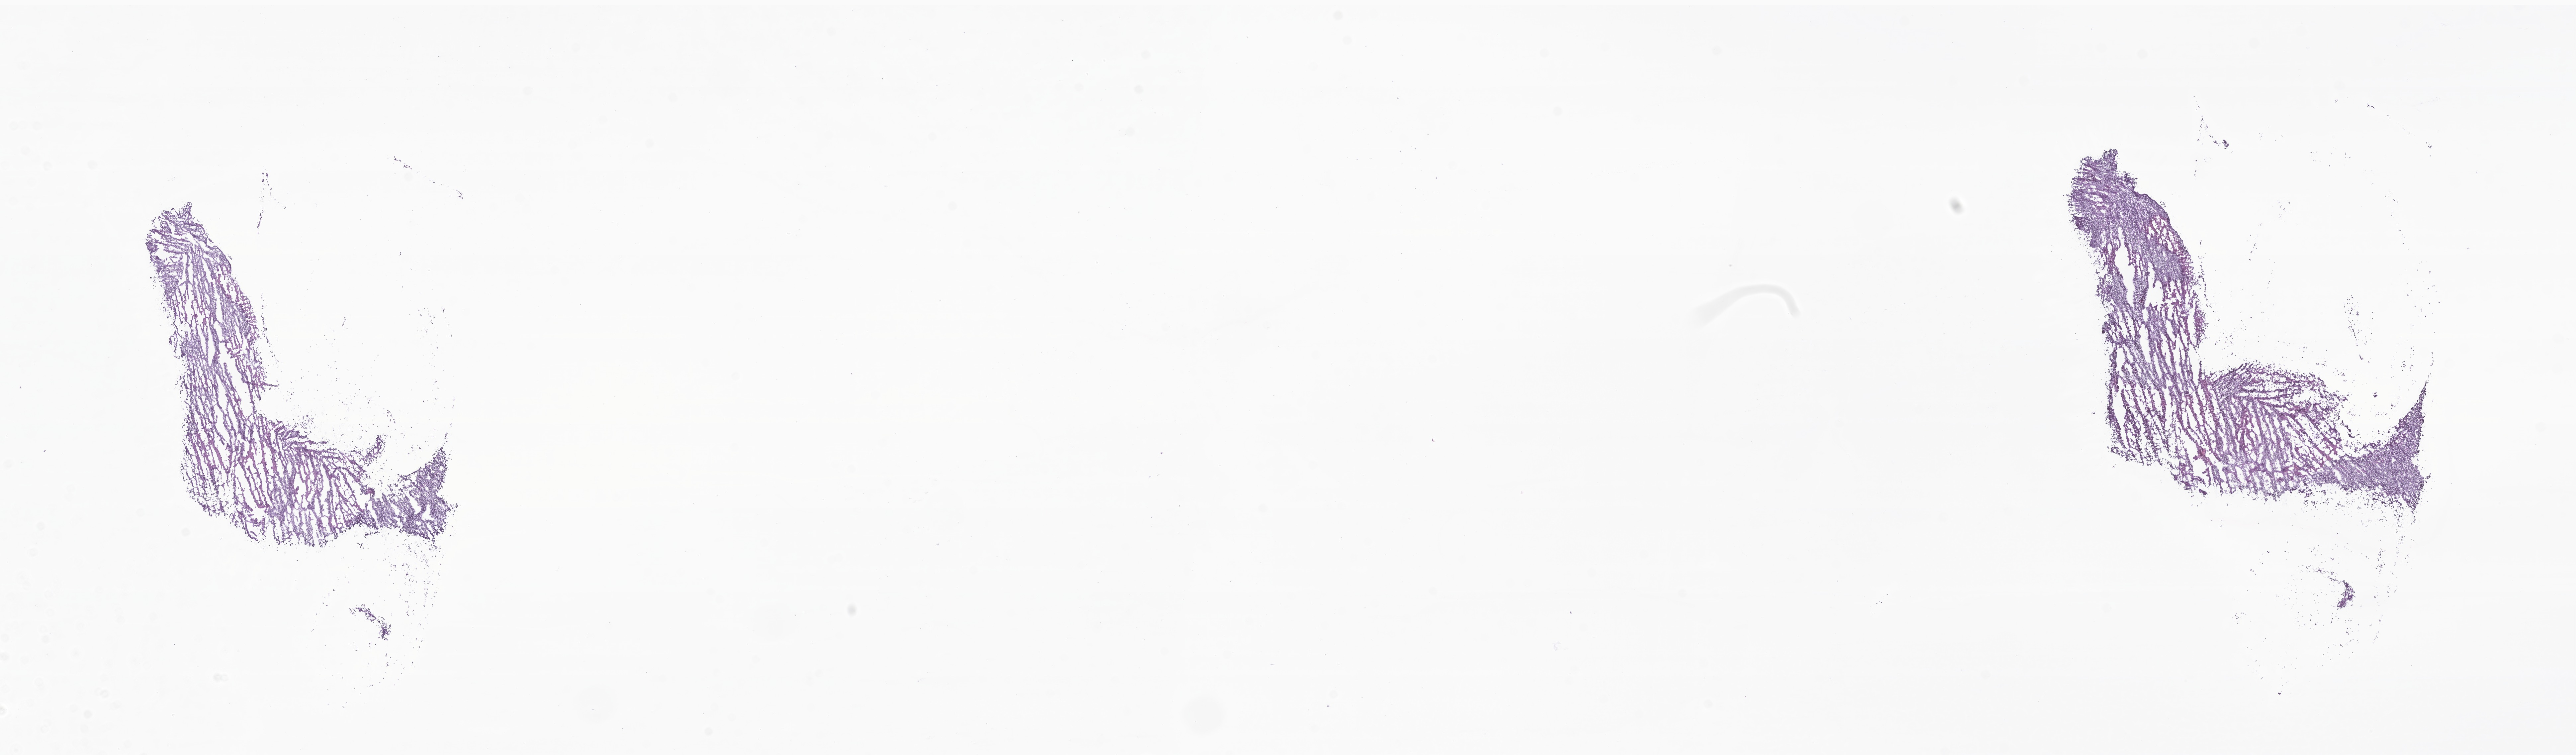
Haematoxylin and eosin whole-slide image of tumor tissue from the brain — low-resolution overview of the scanned area, about 32.7 x 9.6 mm. Frozen section (OCT-embedded). Patient male; age 86 months (7 years 2 months).
* recorded diagnosis: Medulloblastoma, NOS